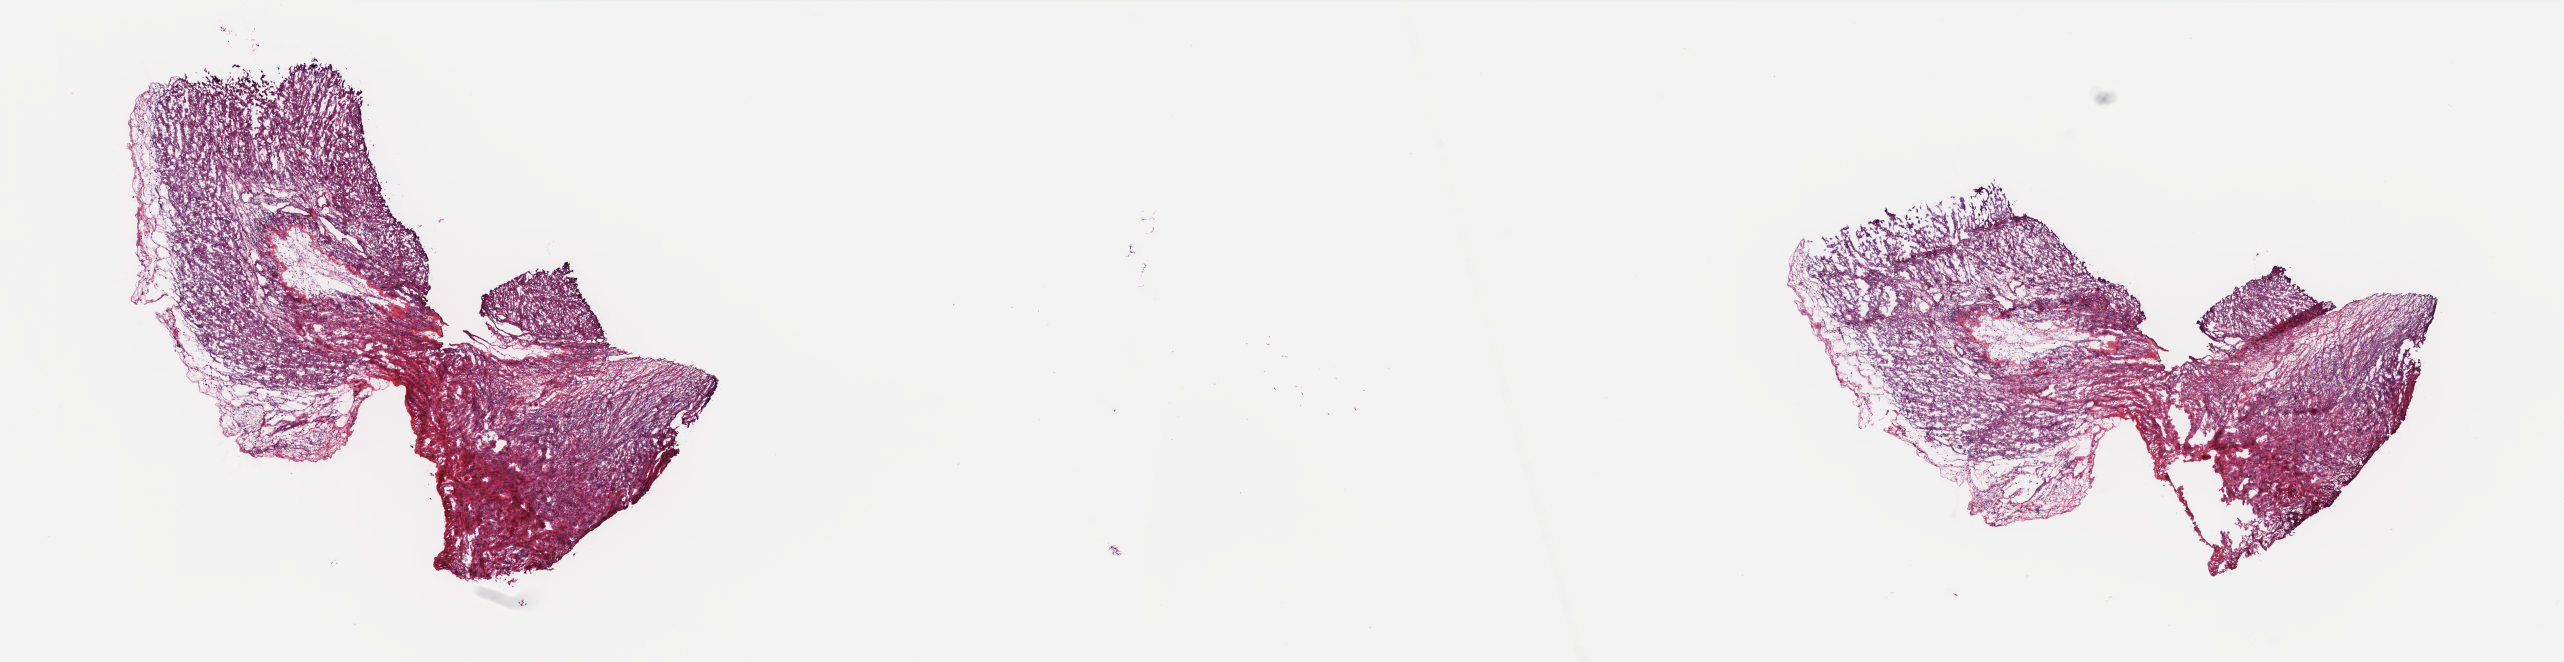
Whole-slide histology image, H&E, a low-resolution overview of the entire scanned area, about 20.7 x 5.3 mm (from a 20x scan). Frozen section. Cervix, solid tissue normal (non-tumour tissue) sample. Female, age 21 years at initial diagnosis. Pathologist review of this section (percent, as recorded): tumour cells 0%, tumour nuclei 0%, normal cells 20%, stromal cells 80%, necrosis 0%. Inflammatory infiltration, as recorded: lymphocyte infiltration 8%, monocyte infiltration 1%, neutrophil infiltration 1%.
- this section: solid tissue normal (non-tumour) sample from the same patient
- patient diagnosis: Squamous cell carcinoma, keratinizing, NOS (cervix uteri)